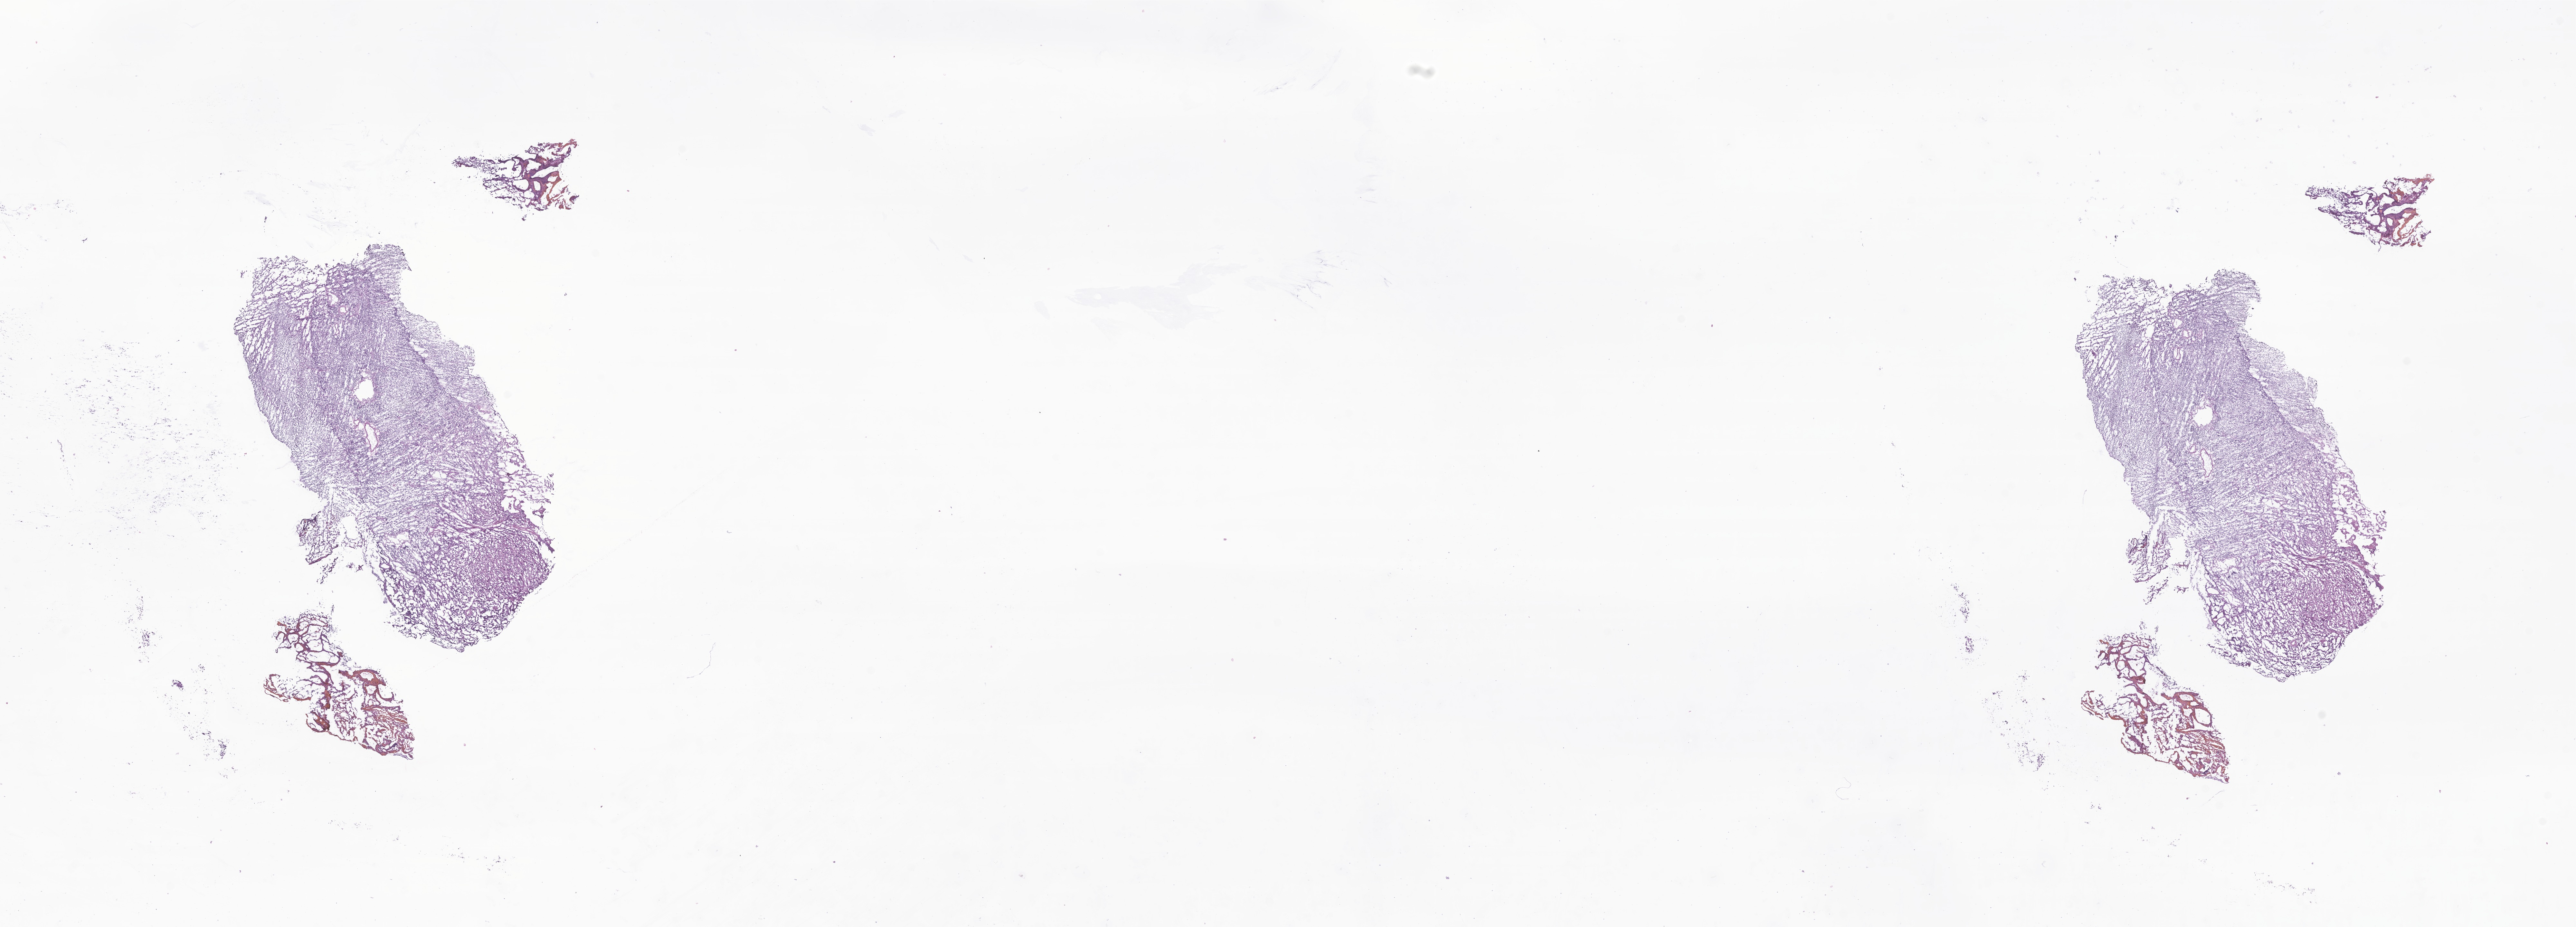
Whole-slide image, haematoxylin and eosin stain of tumor tissue from the cerebellum — whole scanned area (about 33.7 x 12.1 mm) shown as a low-resolution overview. Frozen section. Patient: male, age 201 months (16 years 9 months).
Recorded diagnosis: Medulloblastoma, NOS.